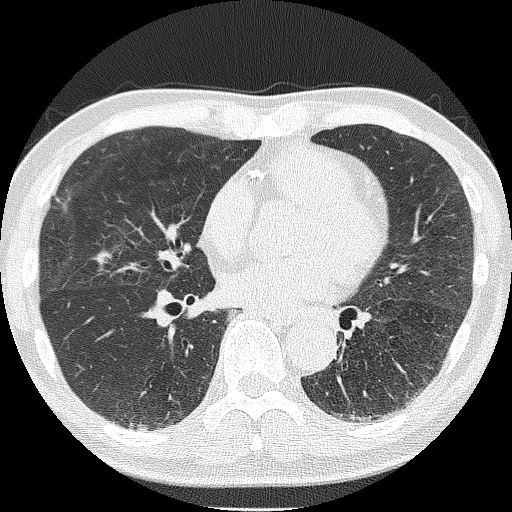
Low-dose screening chest CT, one axial slice. Position 87 of 181 along the scan axis. Reconstruction kernel FC51. 120 kVp. Lung window (W 1500 / L -600 HU). 2 mm slice thickness. 512 × 512 image matrix, field of view 287 × 287 mm.
Annotated regions visible in this slice (manually delineated by an expert):
- lesion 1 (tumor, upper lobe of right lung): bounding box [x1, y1, x2, y2] px = [55, 195, 71, 211]